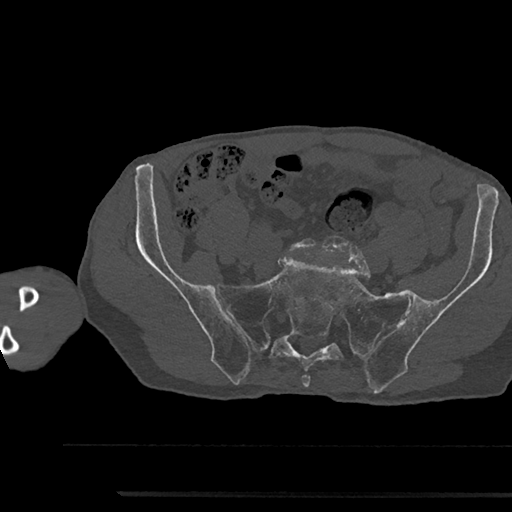
CT including the spine, one axial slice; 120 kVp; bone window (W 1800 / L 400 HU); 0.5 mm slice thickness; 512 × 512 image matrix, field of view 367 × 367 mm. Patient: male, 79 years. Case-level facts recorded for this patient, not image findings: primary cancer: prostate.
Annotated regions visible in this slice (semi-automatically segmented with operator editing):
- L5 vertebra: bounding box [x1, y1, x2, y2] px = [290, 238, 316, 251]